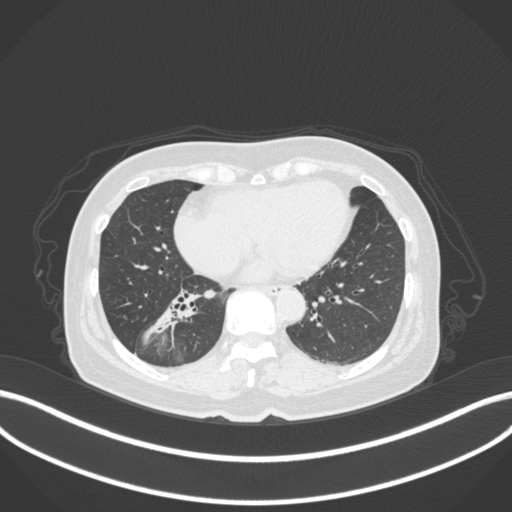
Chest CT, one axial slice. Slice 148 of 429 in the series (ordered by position). Reconstruction kernel B31f. Lung window (W 1500 / L -600 HU). 1 mm slice thickness. 512 × 512 image matrix. Patient: female, 67 years. Case-level facts recorded for this patient, not image findings: clinical TNM (as recorded): T1c N1 M0; histopathological grade: G2-3.
Structures marked on this image (bounding box drawn by a radiologist):
- lung tumour (recorded histology: adenocarcinoma): box from (x=146, y=291) to (x=206, y=346) px